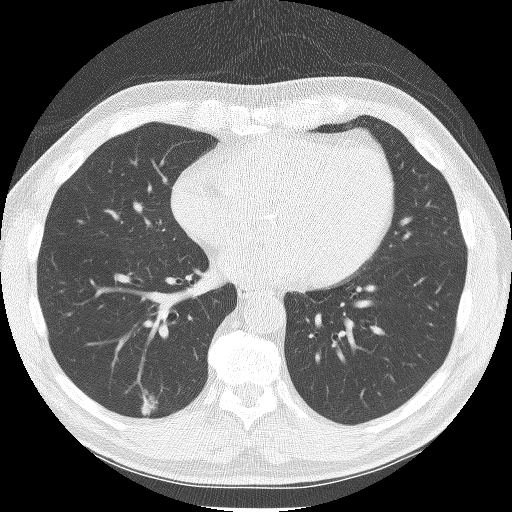
Low-dose screening chest CT, one axial slice. Slice 62 of 150 in the series (ordered by position). Reconstruction kernel BONE. Lung window (W 1500 / L -600 HU). 512 × 512 image matrix, field of view 335 × 335 mm.
Outlined on this slice (manually delineated by an expert):
- lesion 1 (tumor, lower lobe of right lung): bounding box <141,394,158,416> (left, top, right, bottom; pixels)